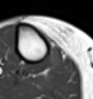
MRI of an extremity soft-tissue mass, one axial slice; slice 34 of 54 in the series (ordered by position); MR volume resampled by the dataset authors to the PET/CT grid (not the native acquisition matrix); 3.27 mm slice thickness; 93 × 99 image matrix, field of view 91 × 97 mm. Female patient. Case-level facts recorded for this patient, not image findings: histological type: undifferentiated – high grade; grade: high; site of the primary tumour: right thigh.
Outlined on this slice (expert contour drawn on MRI and transferred to this co-registered scan by the dataset authors):
- gross tumour volume (mass): bounding box [x1, y1, x2, y2] px = [47, 45, 64, 69]